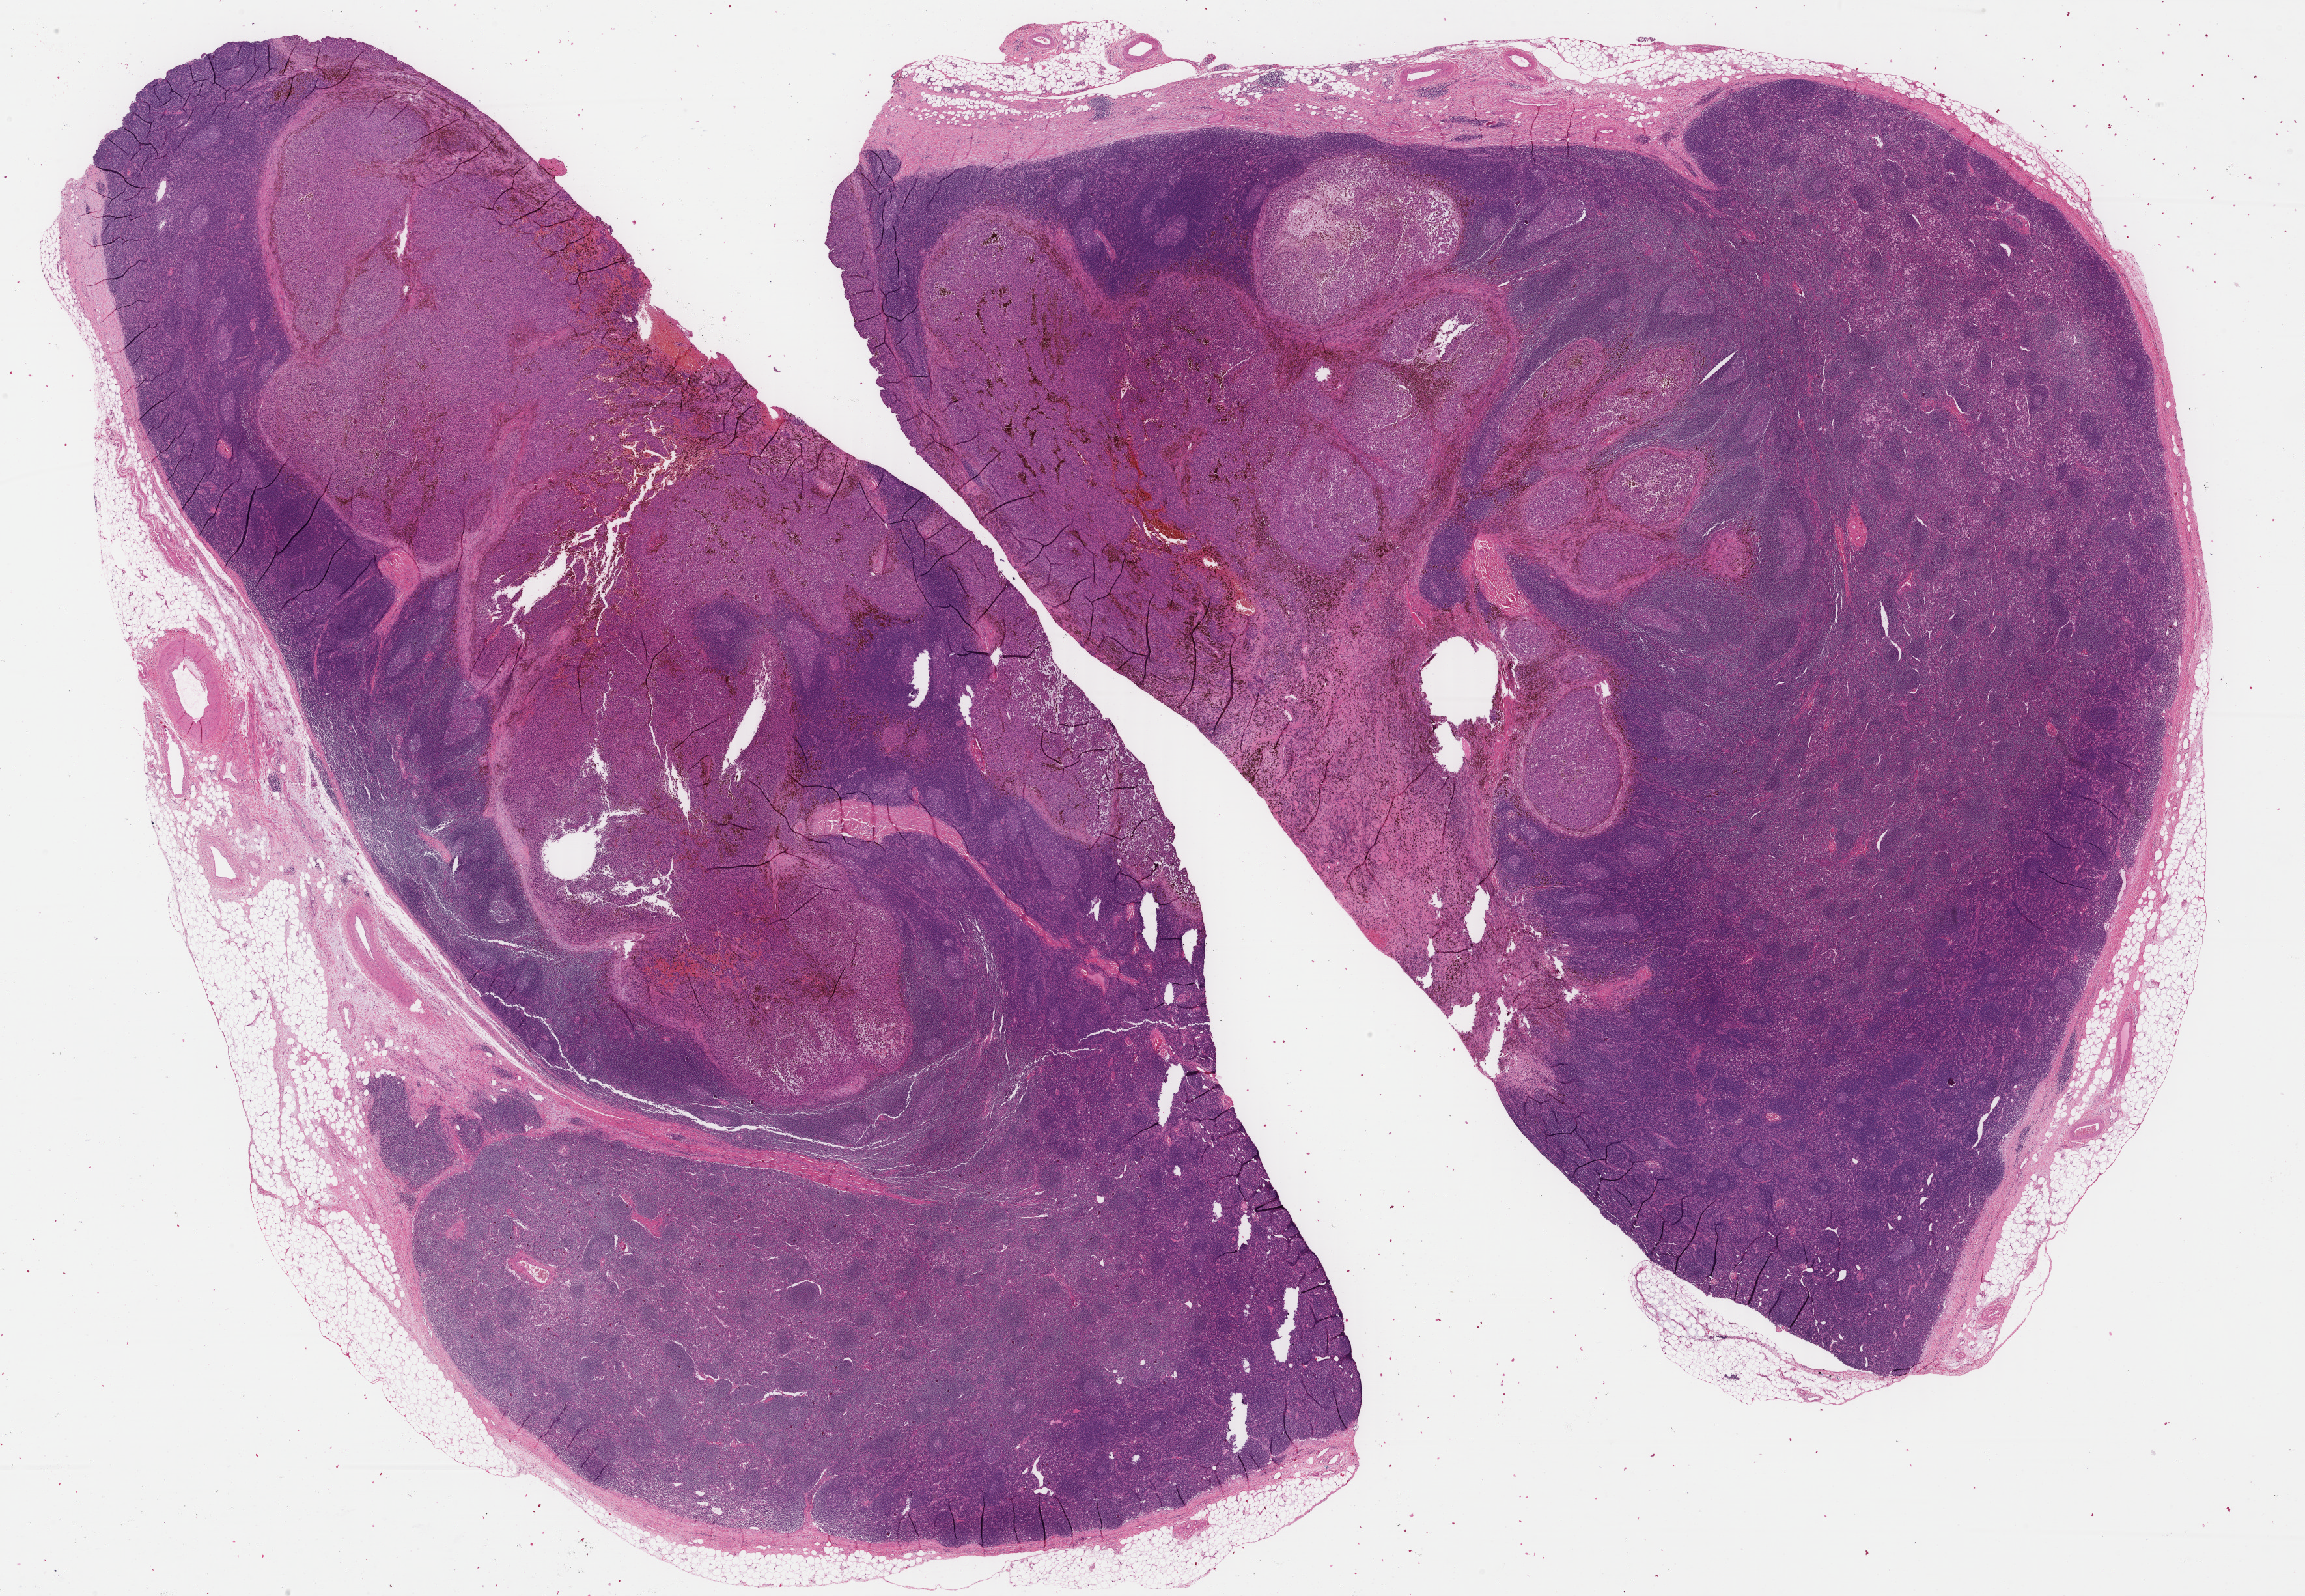
Digitized H&E-stained tissue section (whole slide) — shown as a low-resolution overview of the whole scanned area (about 28.1 x 19.5 mm, slide scanned at 40x). FFPE section. Skin, primary tumour sample. Female patient; age at initial diagnosis 46 years.
Diagnosis: Malignant melanoma, NOS.